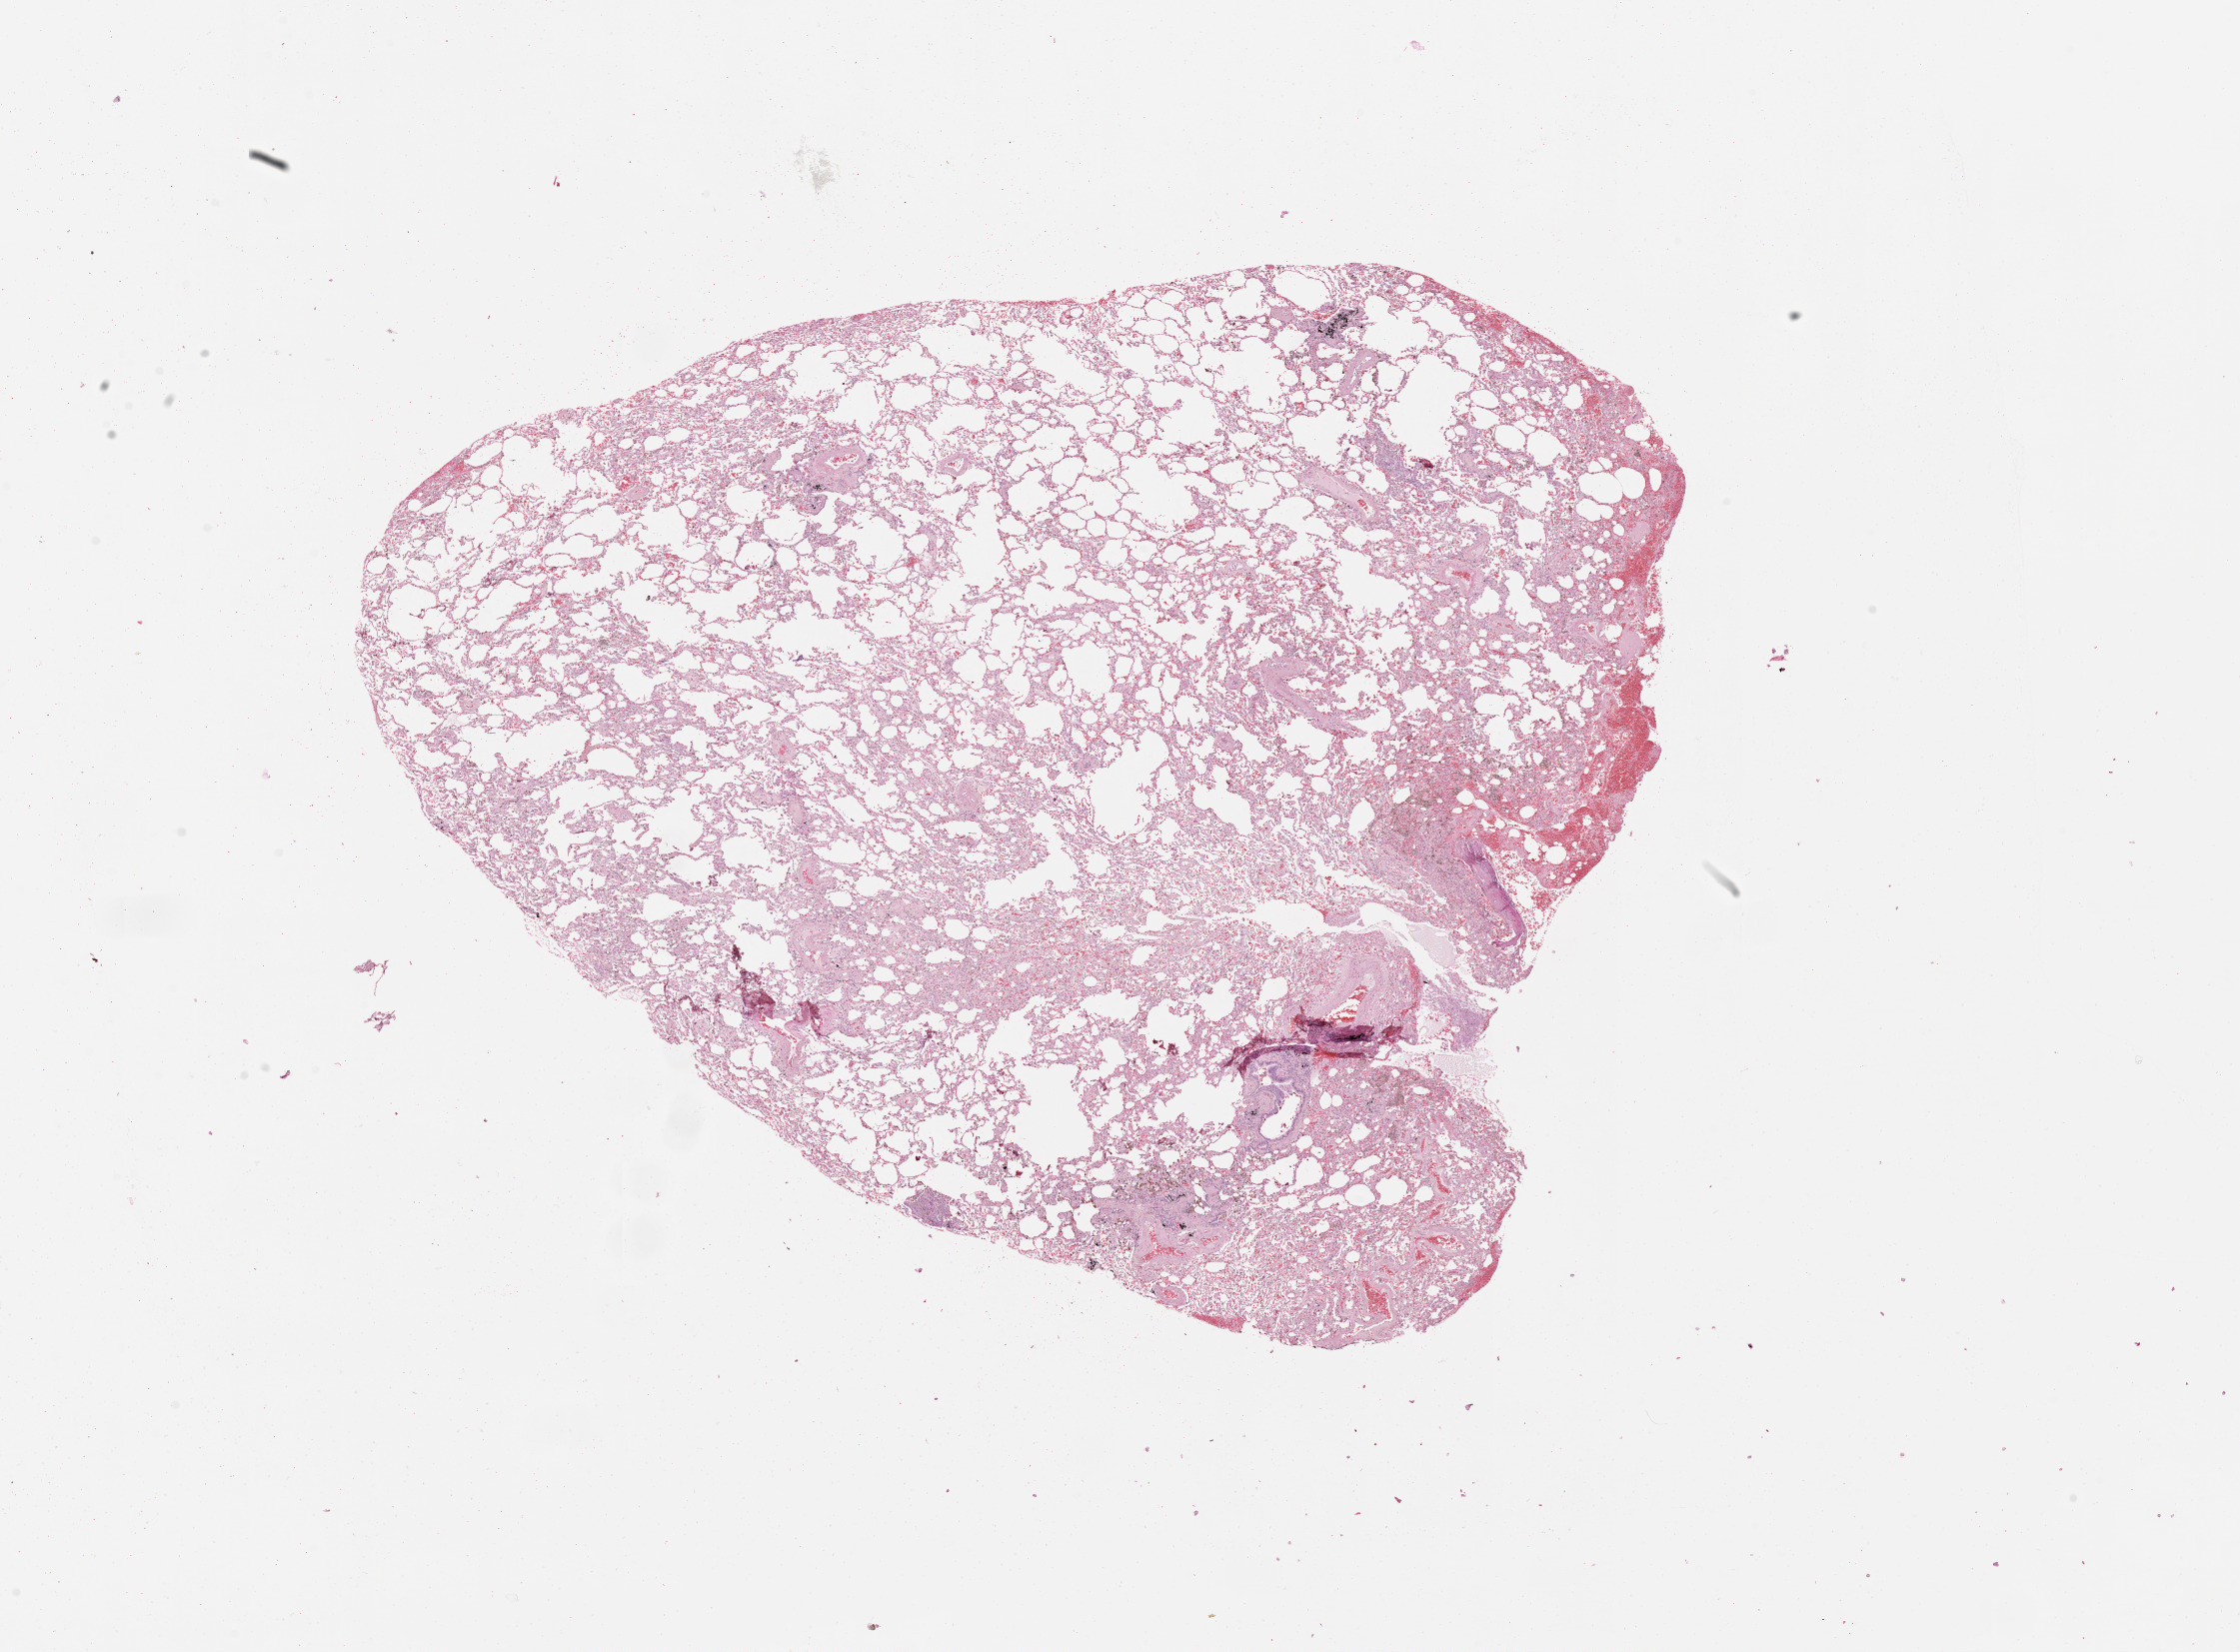
Whole-slide histology image, H&E-stained, low-resolution overview of the scanned area, about 18.0 x 13.3 mm (from a 20x scan), normal (non-tumour) tissue sample, lung. Patient: male, age 56 years.
- this section: normal (non-tumour) tissue from the same patient
- patient diagnosis (cohort enrolment): squamous cell carcinoma (lung)